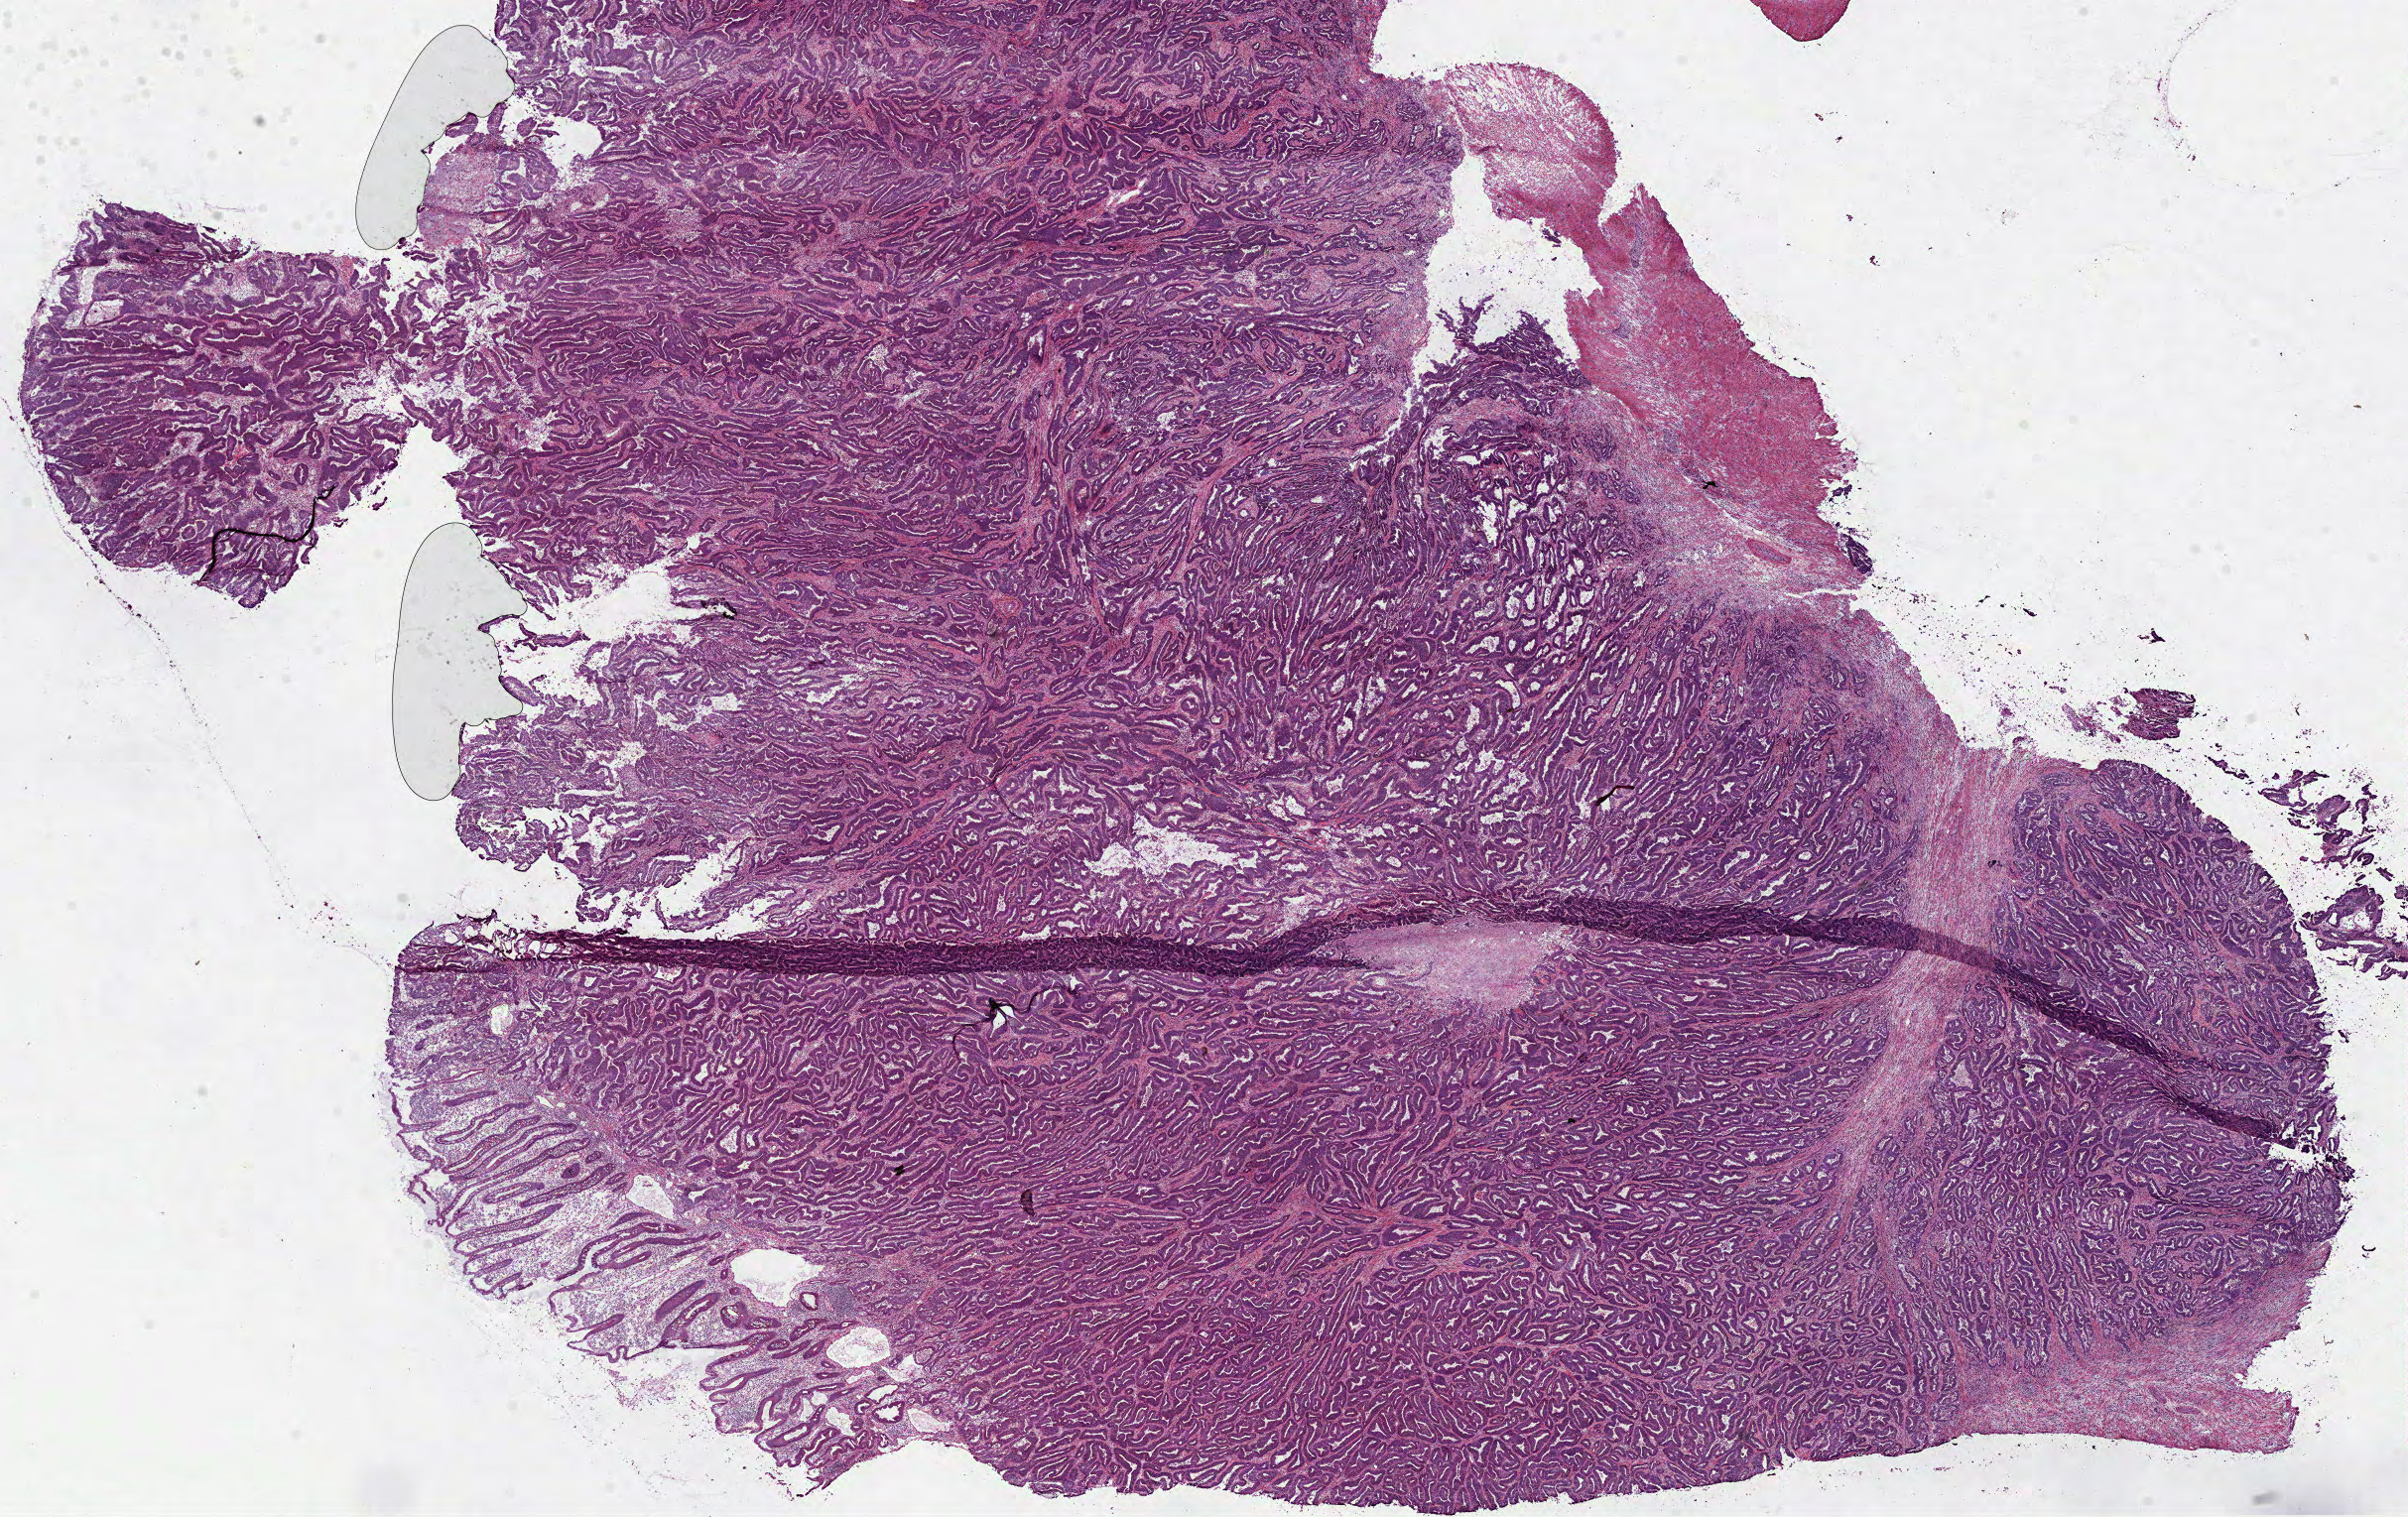
Whole-slide histology image, H&E-stained — whole scanned area (about 19.6 x 12.3 mm, slide scanned at 40x) shown as a low-resolution overview. Frozen section from the bottom of the tissue portion. Colon, primary tumour sample. Patient: male, age at initial diagnosis 35 years. Slide review estimates, as recorded: tumour cells 75%, tumour nuclei 80%, normal cells 8%, stromal cells 12%, necrosis 5%.
Diagnosis: Adenocarcinoma, NOS. AJCC pathologic stage: IVB (7th edition).